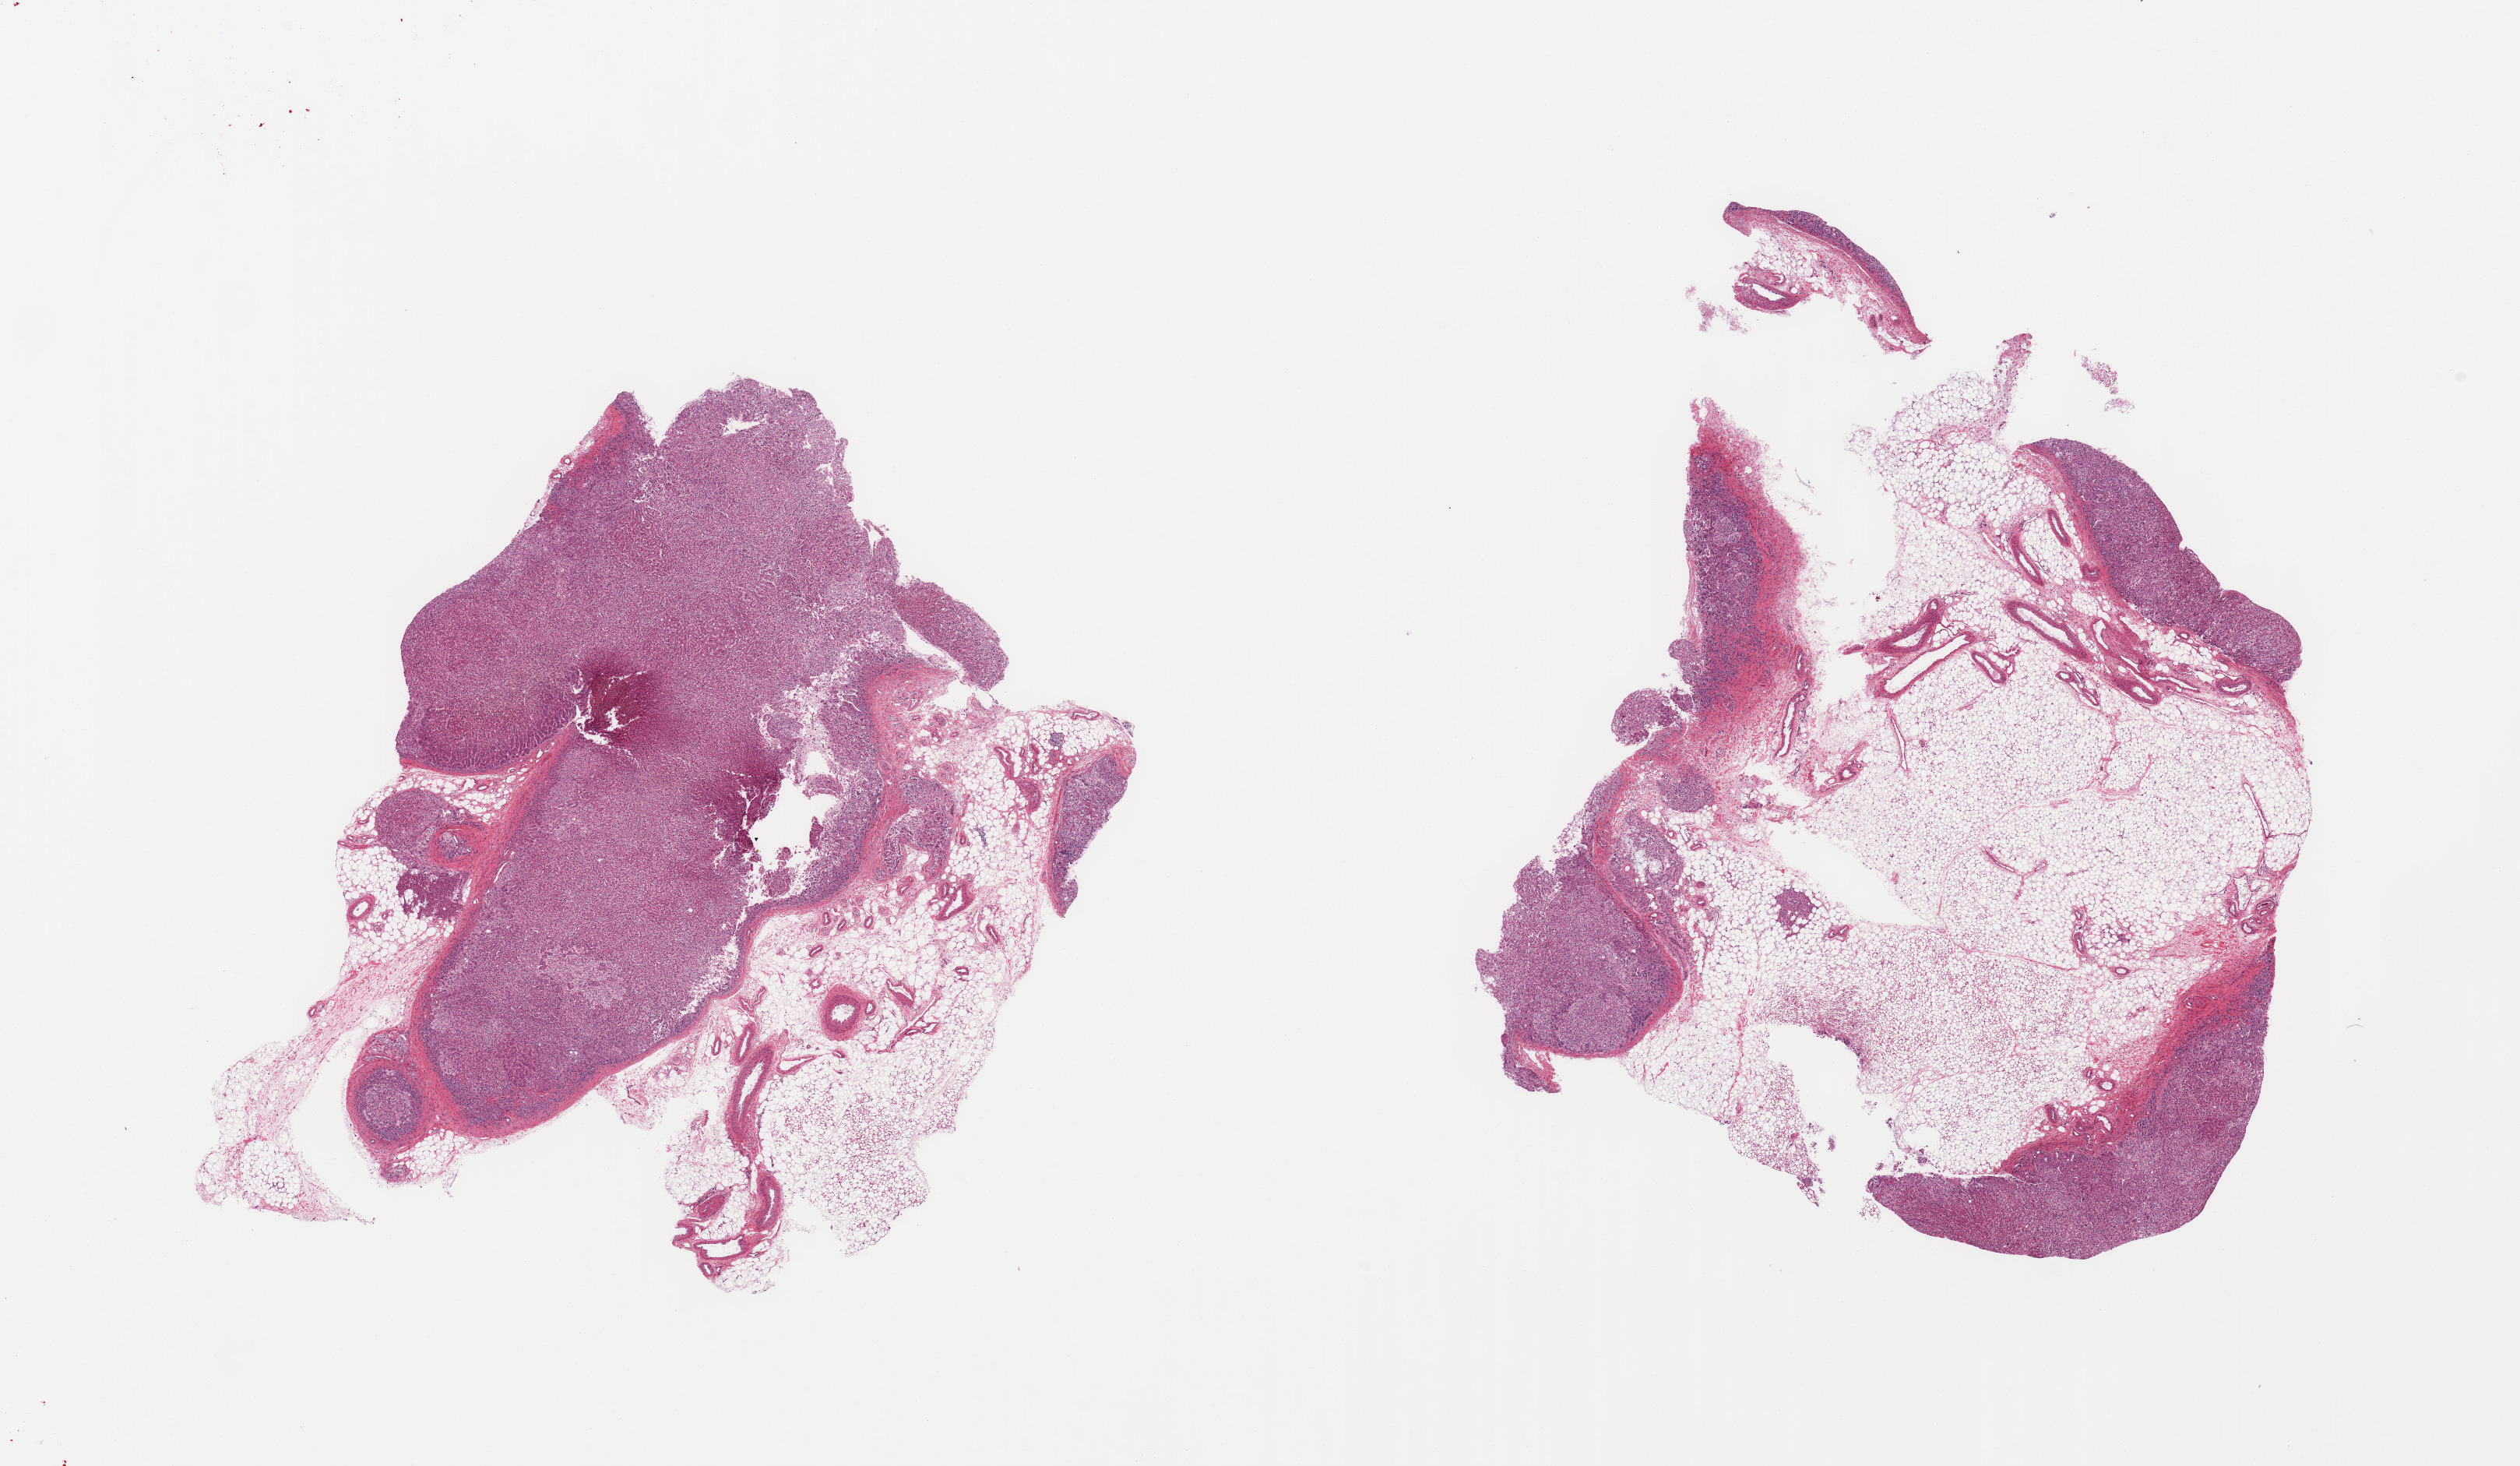
Digitized H&E-stained section, brightfield, low-resolution overview of the scanned area, about 25.6 x 14.9 mm; PAXgene-fixed, paraffin-embedded tissue; target tissue: adrenal gland; tissue donor sample. Donor: female.
Review note (as recorded): 2 pieces; 70% external fat in 1, 40% fat in other.